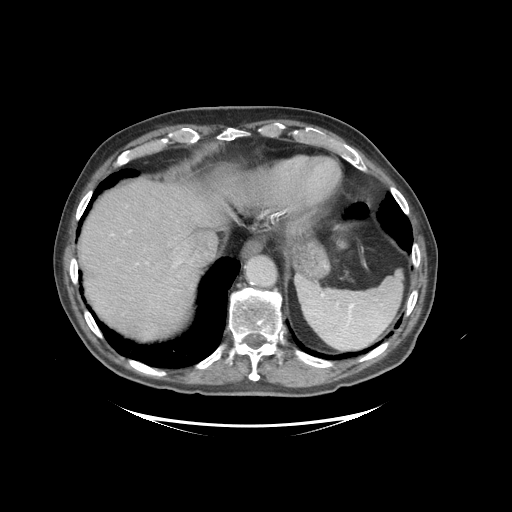
Contrast-enhanced abdominal CT (liver protocol), one axial slice. Slice 81 of 99 in the series (ordered by position). Soft-tissue window (W 400 / L 40 HU). 2.5 mm slice thickness. 512 × 512 image matrix, field of view 460 × 460 mm. Case-level facts recorded for this patient, not image findings: diagnosis: hepatocellular carcinoma (patient treated with transarterial chemoembolisation; whether this scan precedes or follows treatment is not stated here); TNM stage (as recorded): Stage-I; Child-Pugh class: A; tumour differentiation: moderately differentiated.
Outlined on this slice (semi-automatic segmentation, software-assisted and operator-edited):
- liver parenchyma outside the tumour (the mass and vessels are separate outlines, so this box may not span the whole liver): bounding box <78,170,256,340> (left, top, right, bottom; pixels)
- liver vessels: <111,231,182,265>